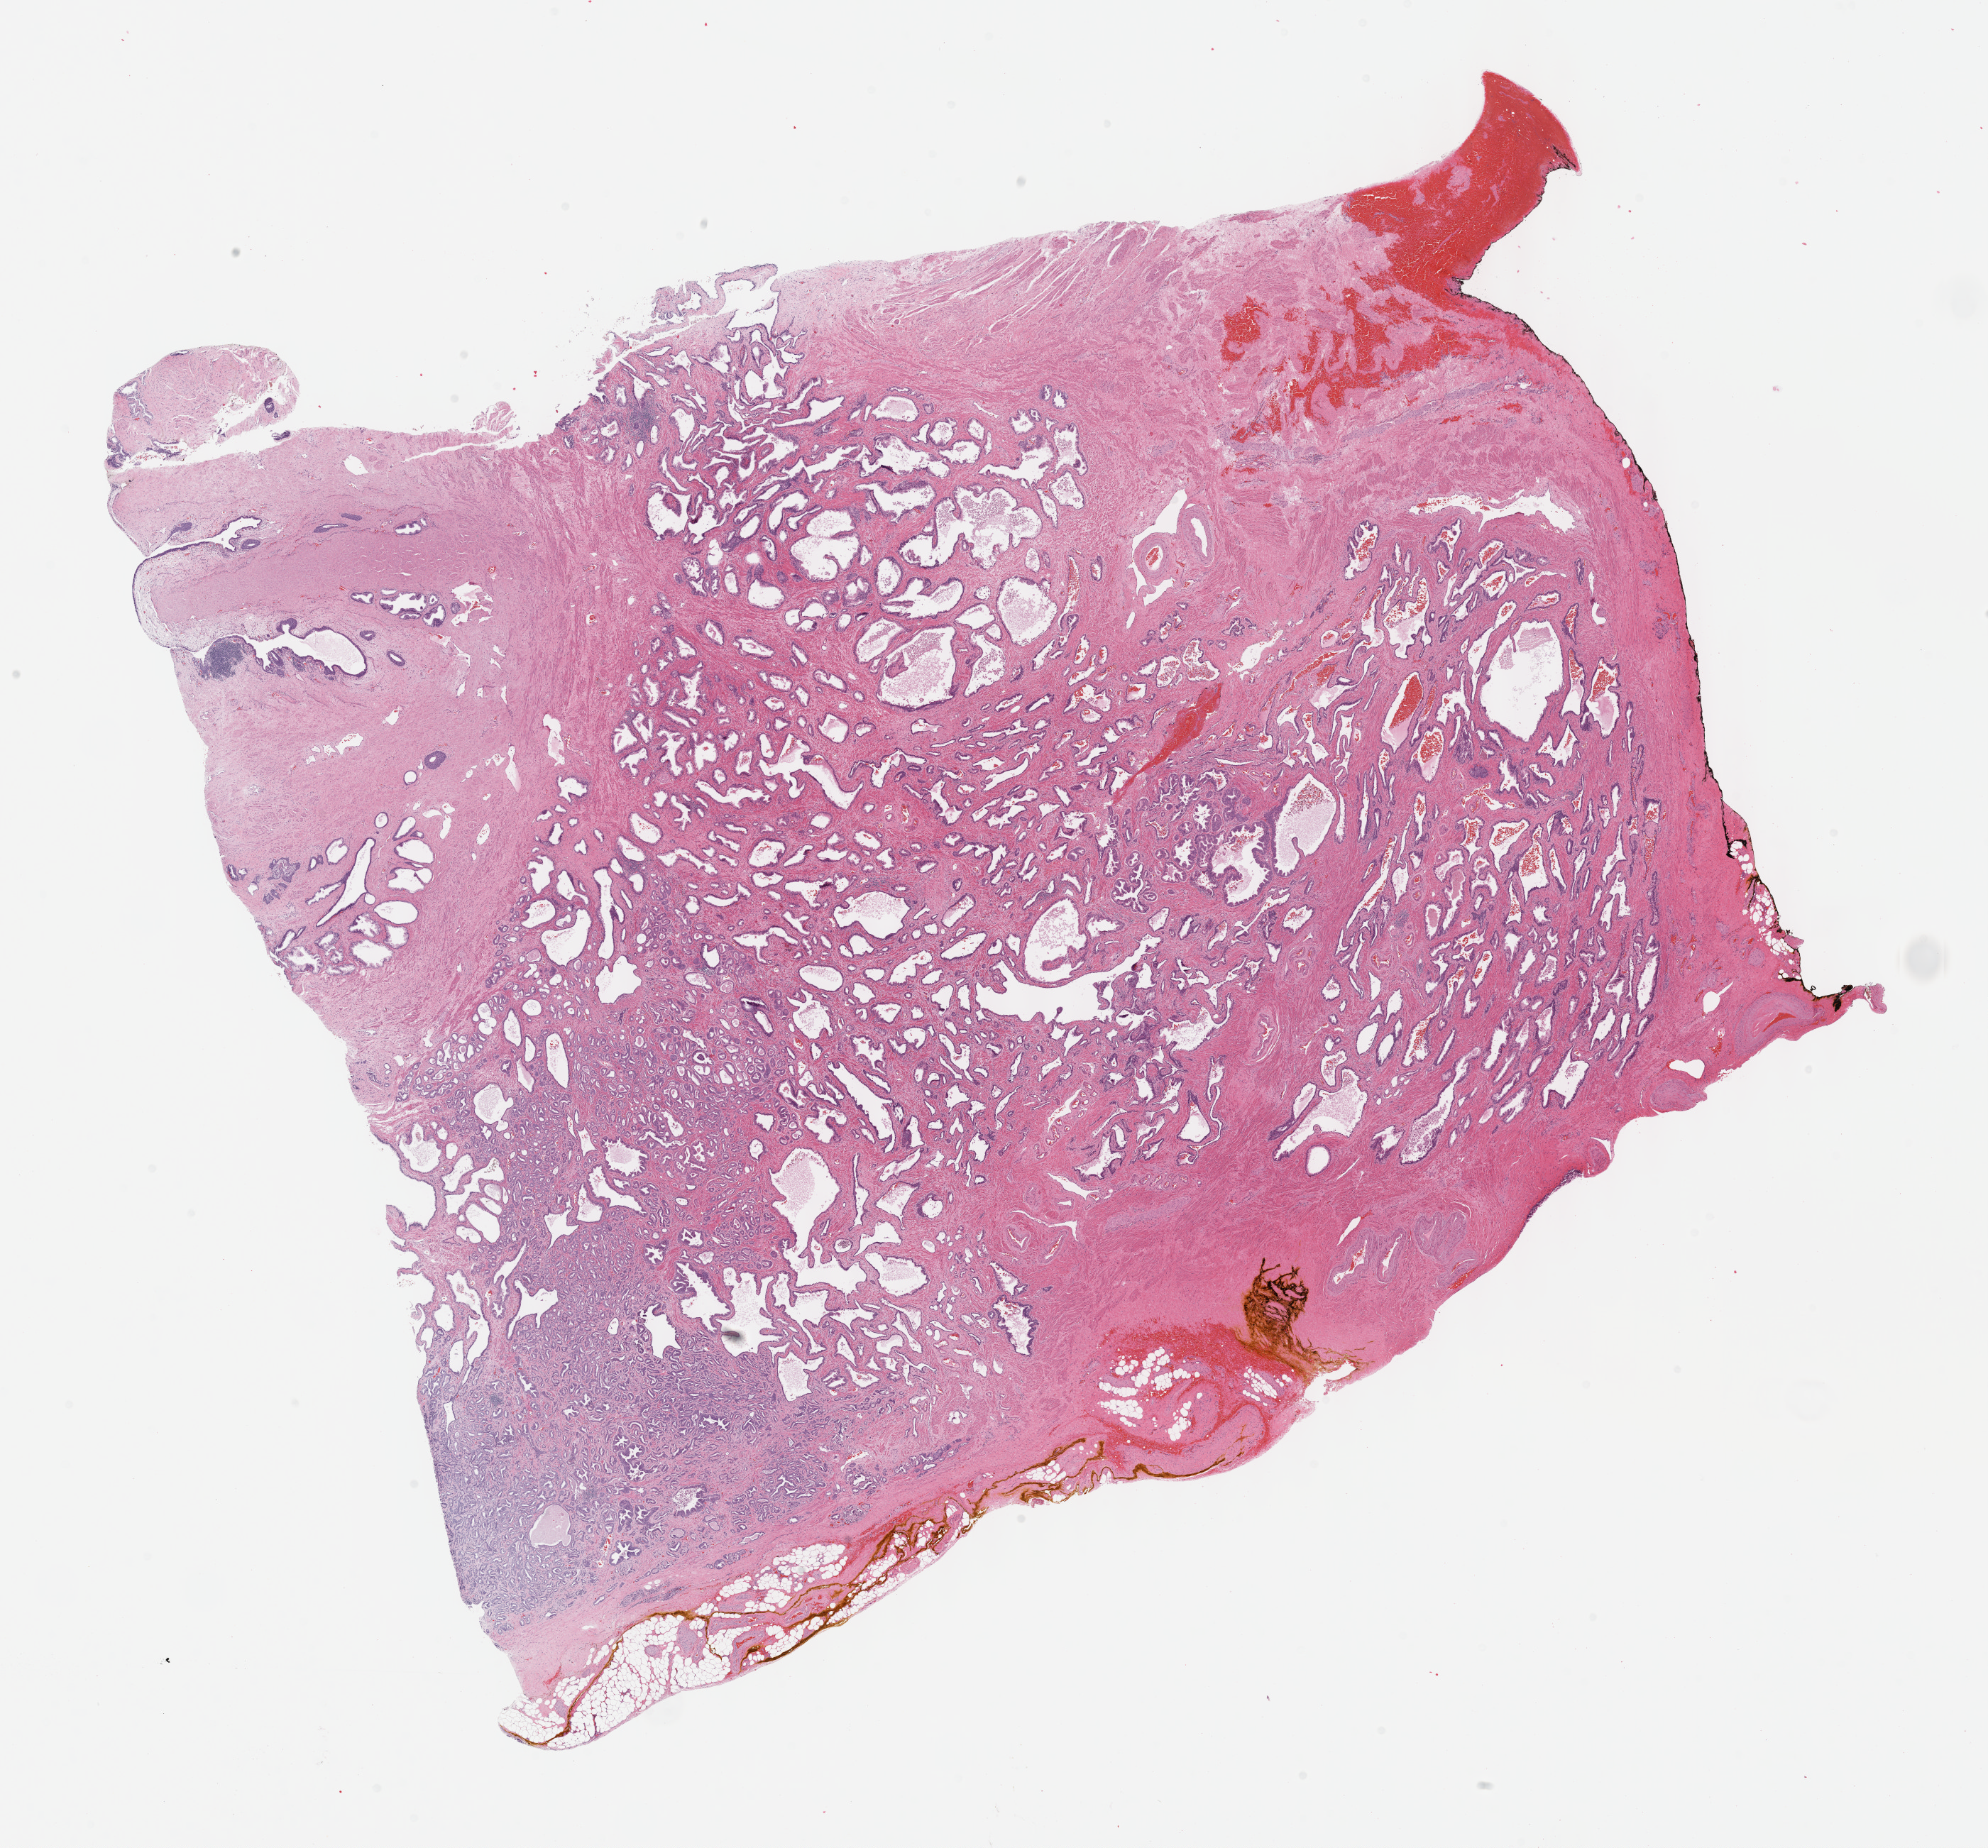
H&E whole-slide image — shown as a low-resolution overview of the whole scanned area (about 22.7 x 21.1 mm, from a 40x scan); FFPE section; sample: primary tumour, prostate. Male, age 68 years at initial diagnosis. Gleason score: 7 (4+3).
- lymph nodes positive (case pathology): 0 of 6 examined
- diagnosis: Acinar cell carcinoma (prostate gland)